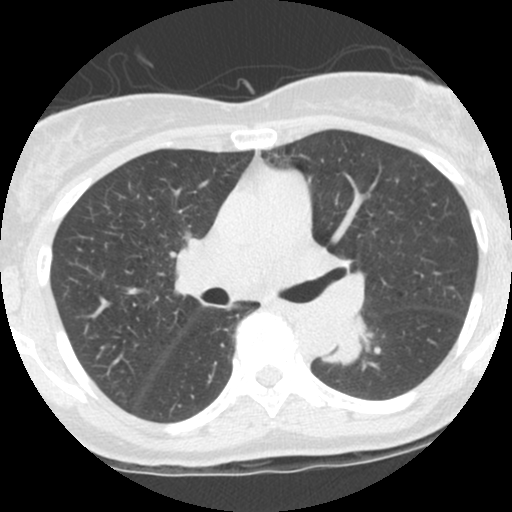
Low-dose screening chest CT, one axial slice; slice 66 of 115 in the series (ordered by position); lung window (W 1500 / L -600 HU); 512 × 512 image matrix.
Structures marked on this image (outlined manually by an expert reader):
- lesion 1 (tumor, lower lobe of left lung): bounding box (x1, y1, x2, y2) in pixels: (323, 319, 366, 364)